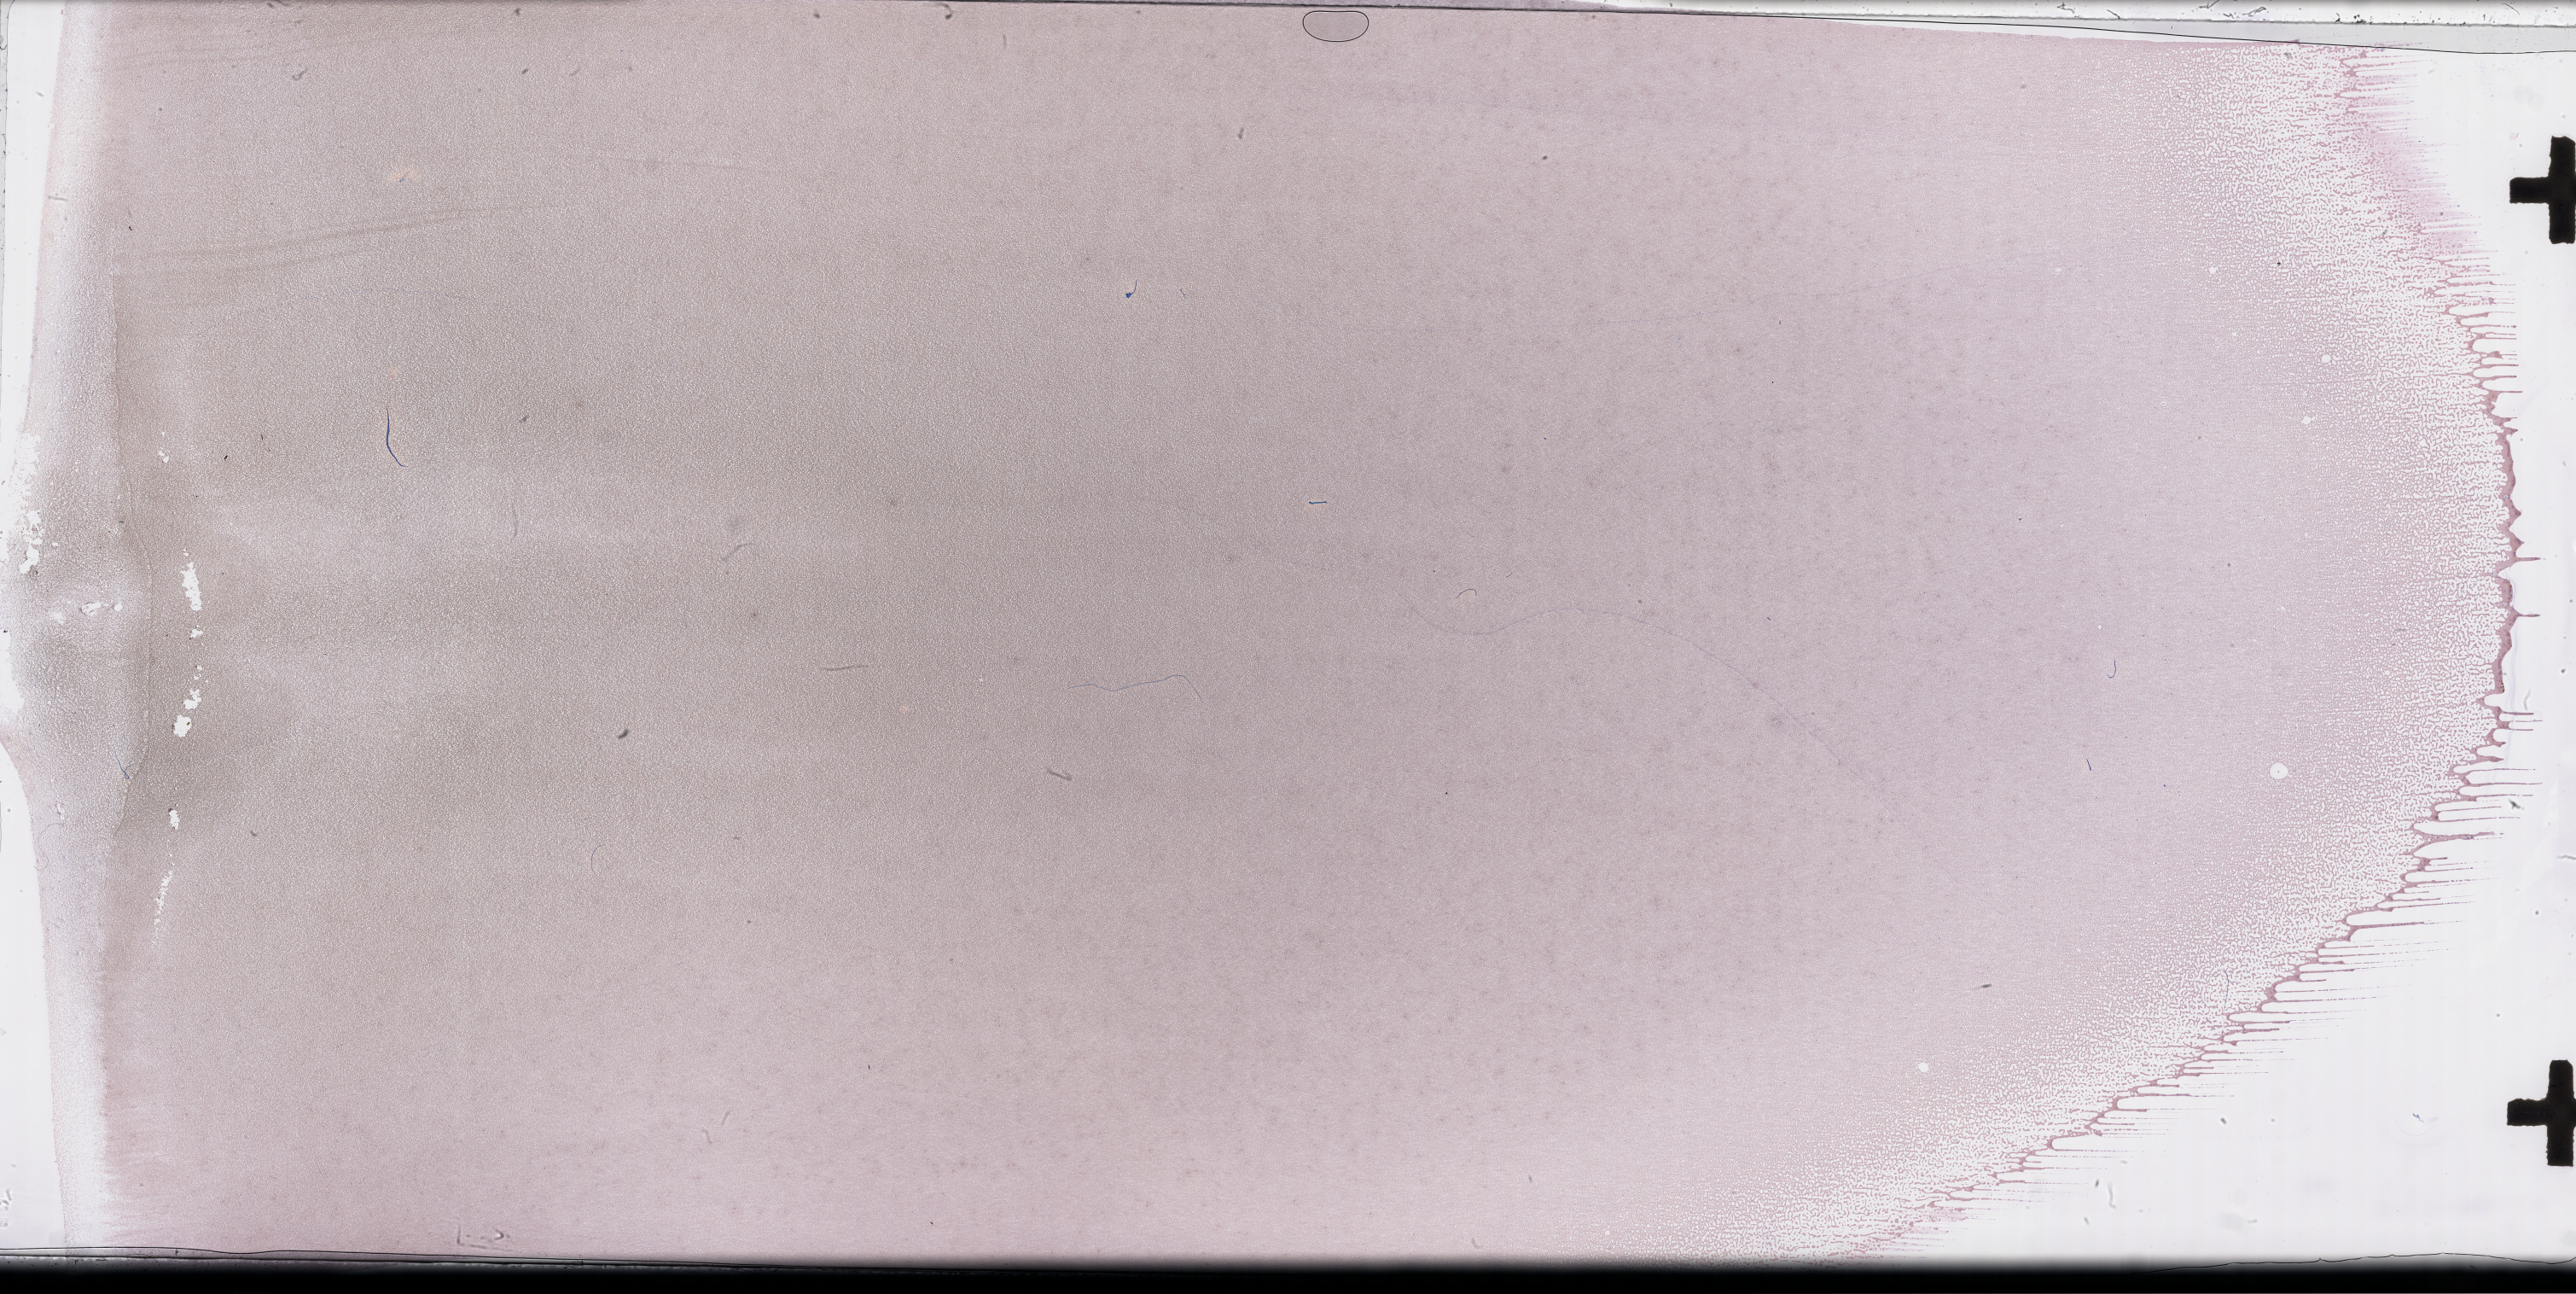
Whole-slide image of a whole blood smear, Wright–Giemsa stain — low-resolution overview of the scanned area, about 48.8 x 24.5 mm; smear from an EDTA sample. Patient sex: male.
- from a patient with: Plasma Cell Myeloma